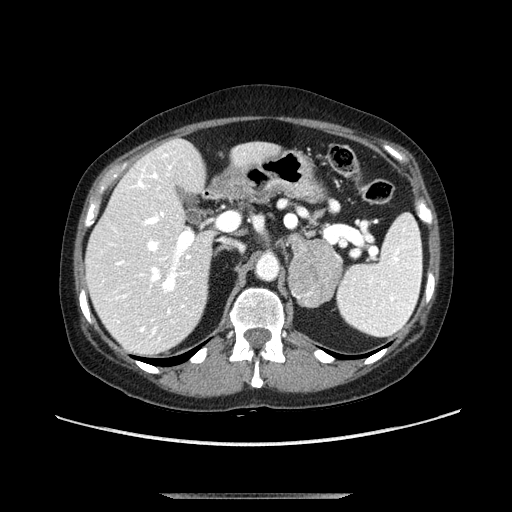
Contrast-enhanced abdominal CT, one axial slice. Position 67 of 107 along the scan axis. Soft-tissue window (W 400 / L 40 HU). 2.5 mm slice thickness. 512 × 512 image matrix. Female patient. From the clinical record (not read from this slice): diagnosis: adrenocortical carcinoma; tumour side: left adrenal; tumour size at pathology: 7.5 cm; Ki-67 index: 9 %; stage (as recorded): 3.
Annotated regions visible in this slice (semi-automatic segmentation, software-assisted and operator-edited):
- mass: bounding box (x1, y1, x2, y2) in pixels: (288, 238, 345, 308)